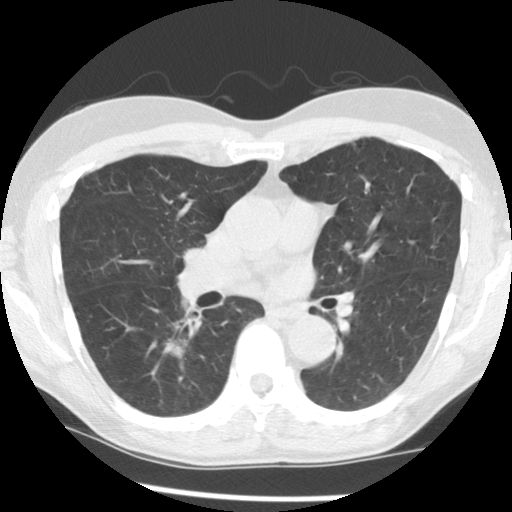
Axial slice from a low-dose chest CT screening exam. Third annual screen. Lung window (W 1500 / L -600 HU). Slice 77 of 145 in the series. Male participant, aged 65 years at enrolment. Current smoker at enrolment.
Expert-annotated lung lesion, box from (x=145, y=320) to (x=205, y=376) px. The screening reader recorded 2 non-calcified nodules or masses ≥4 mm on this exam (left lower lobe, right lower lobe); which of them this box marks is not recorded. Participant outcome: lung cancer diagnosed 116 days after this screen — adenocarcinoma, NOS, right lower lobe, poorly differentiated (G3), stage IA (AJCC 6th edition), 18 mm at pathology.